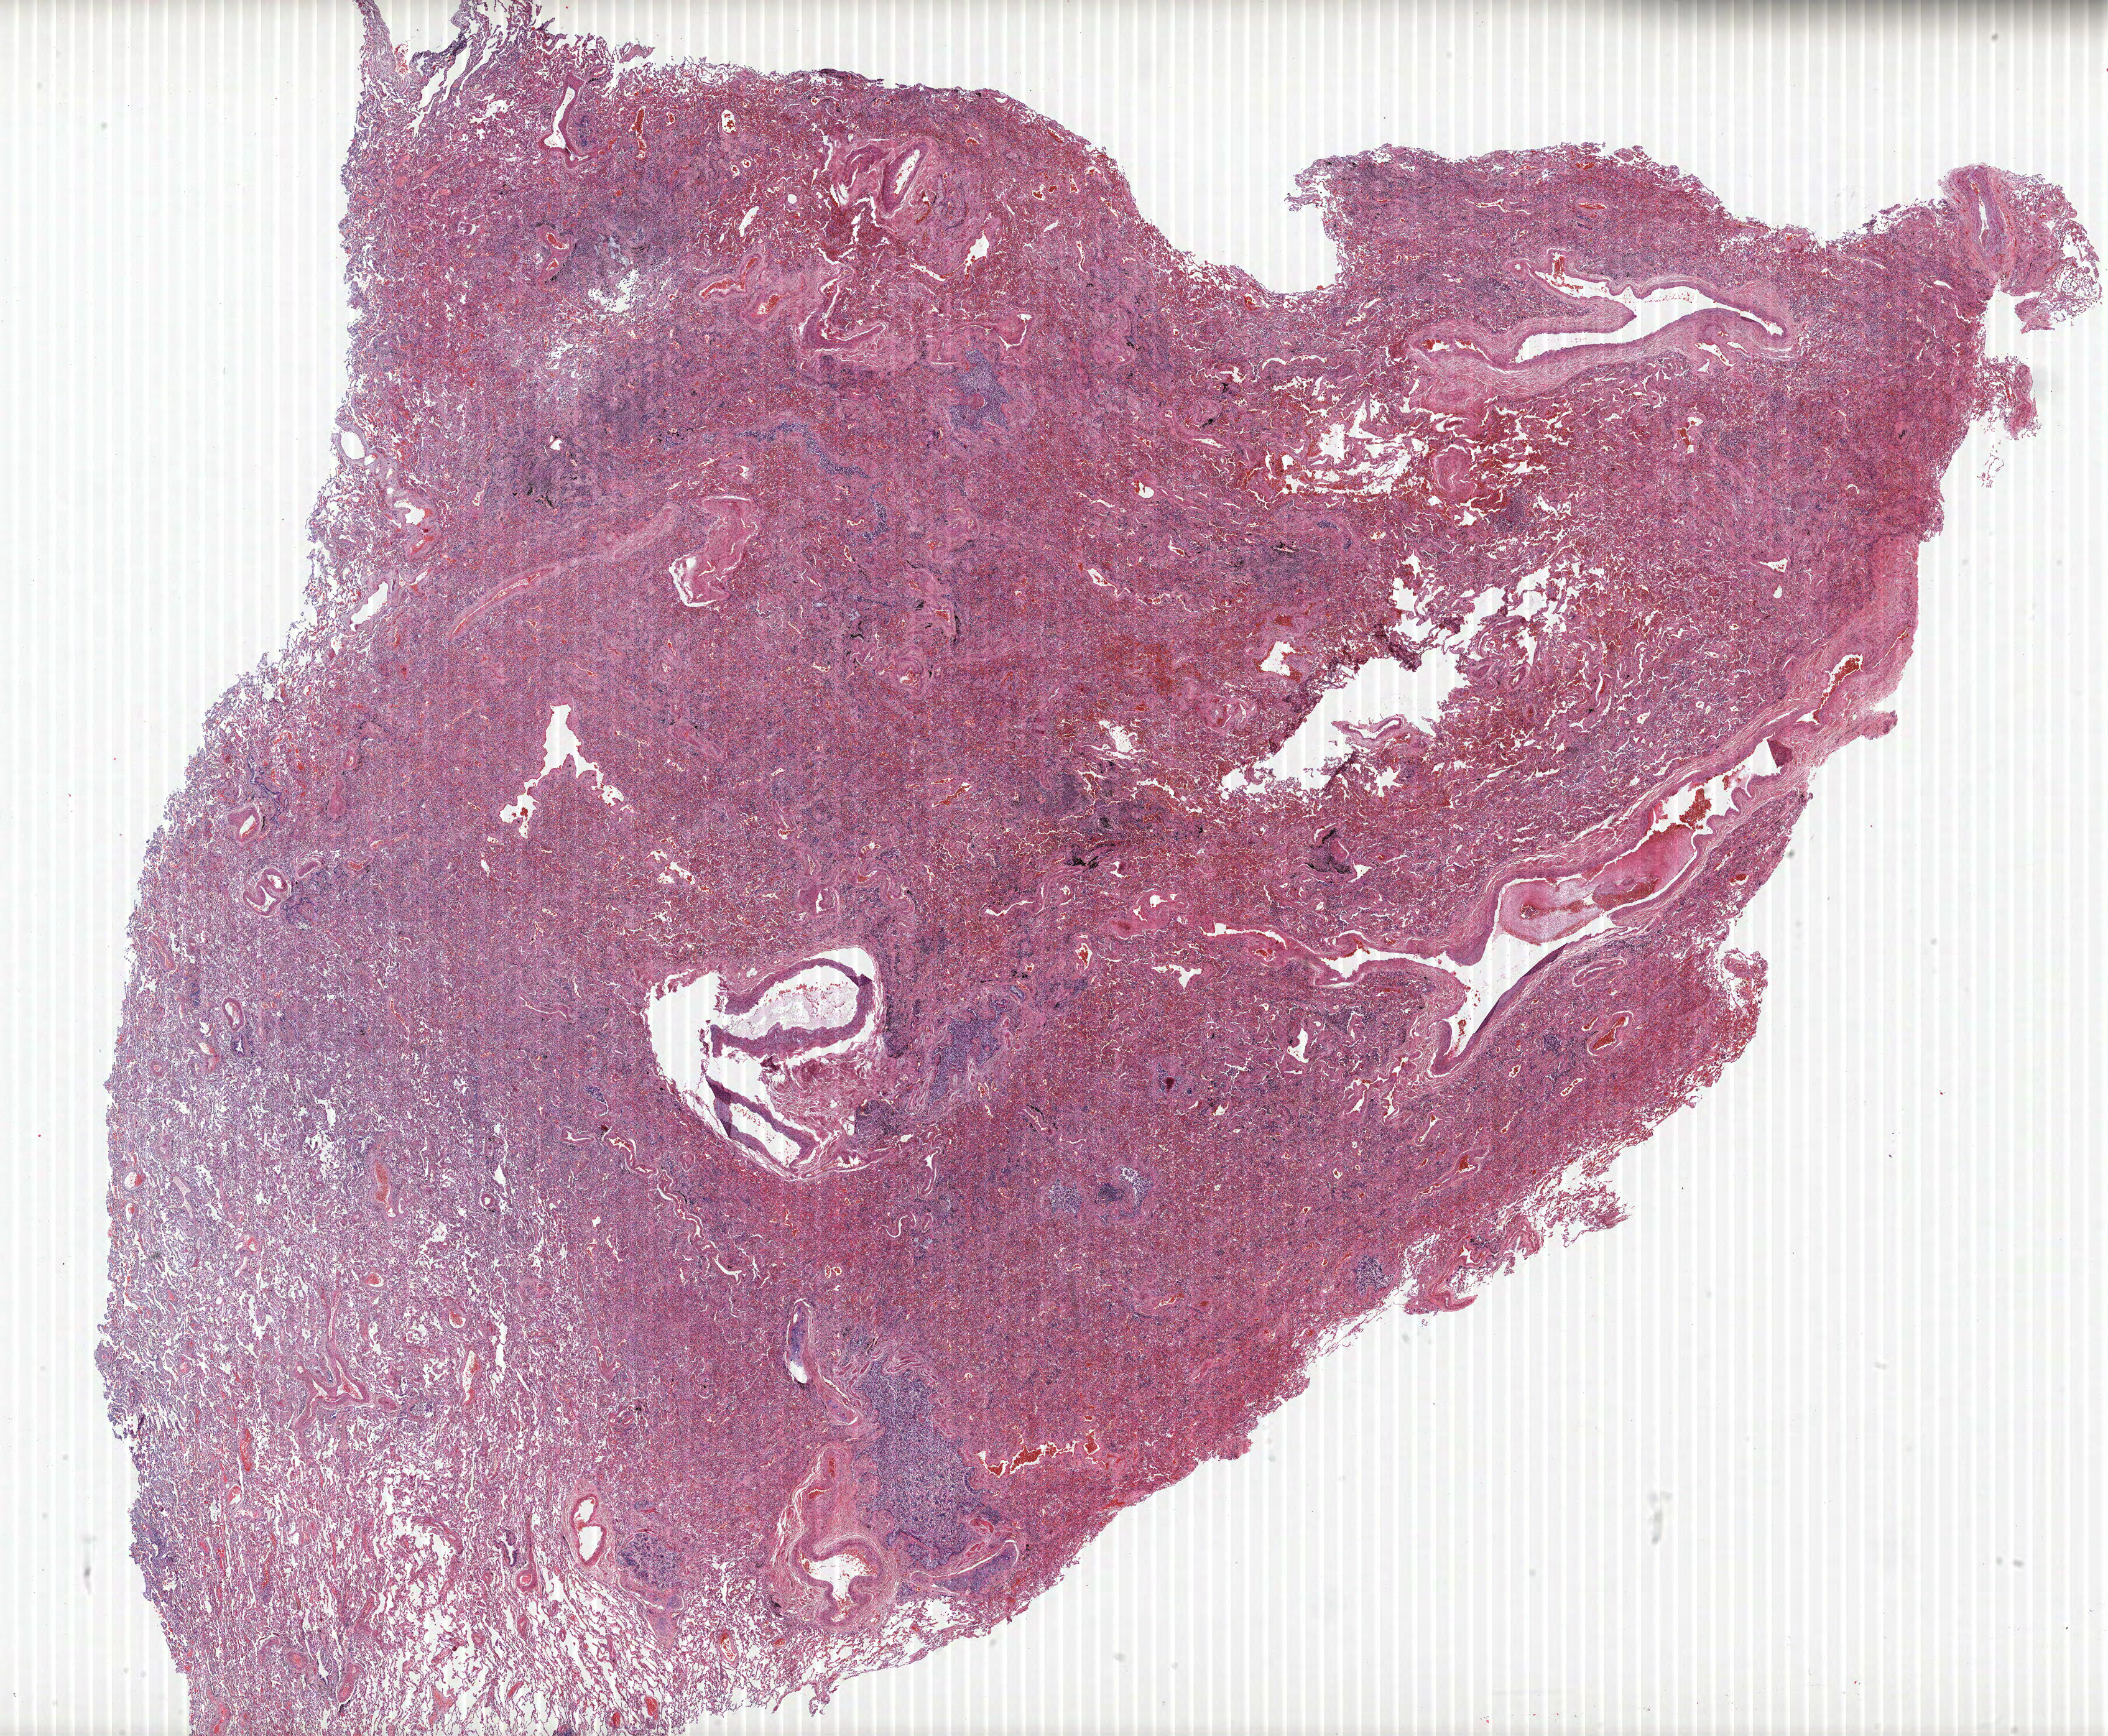
Whole-slide histology image, Hematoxylin and eosin (H&E) stained, shown as a low-resolution overview of the whole scanned area (about 27.1 x 22.3 mm), FFPE section, lung. Male patient, aged 58 at enrolment. Current smoker at enrolment. Grade: moderately differentiated (G2).
Stage (AJCC 6th edition): IA. Primary tumour location (clinical record): left lower lobe. Participant's lung-cancer diagnosis: Adenosquamous carcinoma. Tumour size (pathology): 28 mm. ICD-O-3 topography: lower lobe of lung (C34.3).